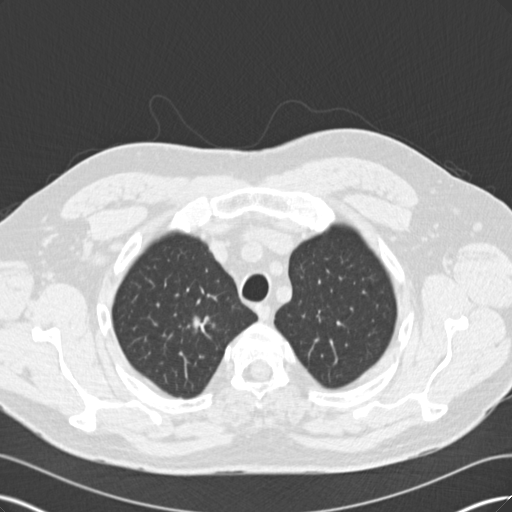
Low-dose screening chest CT, axial slice; baseline annual screen; lung window (W 1500 / L -600 HU); 2 mm slice thickness; 120 kVp; slice 26 of 171 in the series; 512 × 512 image matrix. Male, age 56 years at enrolment.
Expert-annotated lung lesion, bounding box (x1, y1, x2, y2) in pixels: (173, 305, 227, 349). Reader record for this screening exam (exam-level; its link to the box is not recorded): non-calcified nodule or mass ≥4 mm, right upper lobe, 14 × 8 mm, spiculated (stellate) margins. Participant outcome: lung cancer diagnosed 146 days after this screen — adenocarcinoma, NOS, right upper lobe, poorly differentiated (G3), stage IA (AJCC 6th edition), 12 mm at pathology.